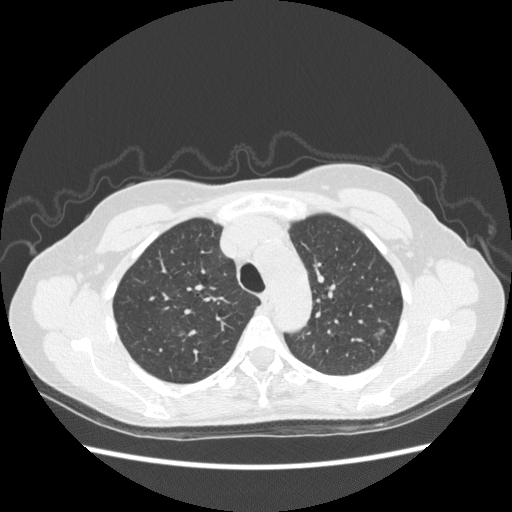
Chest CT (low-dose screening protocol), one axial image; baseline screening round; lung window (W 1500 / L -600 HU); 1.25 mm slice thickness; 120 kVp; slice 73 of 270 in the series; 512 × 512 image matrix, field of view 360 × 360 mm. Female participant, aged 61 years at enrolment. Former smoker at enrolment.
- Lesion marked by an expert reader, bounding box [x1, y1, x2, y2] px = [356, 321, 397, 354].
- Reader record for this screening exam (exam-level; its link to the box is not recorded): non-calcified nodule or mass ≥4 mm, left upper lobe, 7 × 6 mm, poorly defined margins, ground glass attenuation.
- Official screen result: positive, change unspecified: nodule(s) >= 4 mm or enlarging nodule(s), mass(es), or other non-specific abnormalities suspicious for lung cancer.
- Participant outcome: lung cancer diagnosed 484 days after this screen — bronchiolo-alveolar adenocarcinoma, NOS, left upper lobe, well differentiated (G1), stage IA (AJCC 6th edition), 8 mm at pathology.